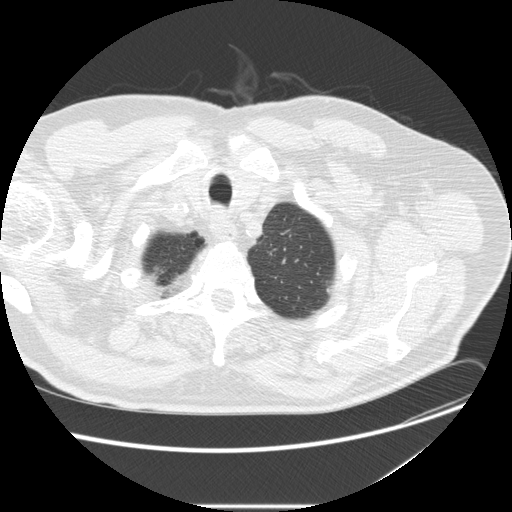
Axial slice from a low-dose chest CT screening exam. Baseline annual screen. Lung window (W 1500 / L -600 HU). Slice 31 of 263 in the series. Male participant, aged 73 years at enrolment.
- Expert-annotated lung lesion, bounding box (x1, y1, x2, y2) in pixels: (319, 277, 349, 304).
- Screening reader's record for this exam: no non-calcified nodule ≥4 mm recorded.